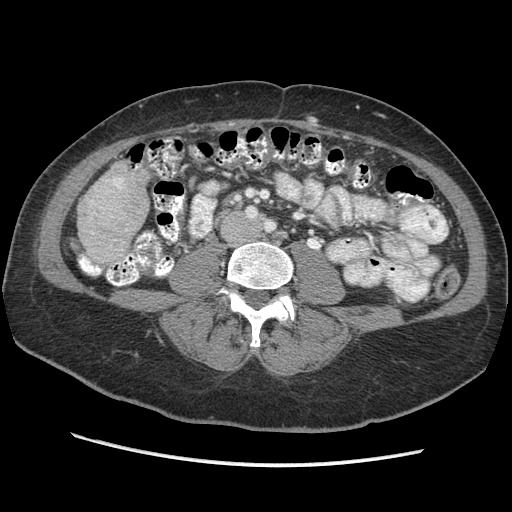
Contrast-enhanced abdominal CT (liver protocol), one axial slice. Slice 86 of 170 in the series (ordered by position). Soft-tissue window (W 400 / L 40 HU). 2.5 mm slice thickness. 512 × 512 image matrix. Case-level facts recorded for this patient, not image findings: diagnosis: hepatocellular carcinoma (patient treated with transarterial chemoembolisation; whether this scan precedes or follows treatment is not stated here); TNM stage (as recorded): Stage-II; Child-Pugh class: A; tumour differentiation: no biopsy; tumour nodularity: multinodular.
Structures marked on this image (semi-automatic segmentation, software-assisted and operator-edited):
- liver parenchyma outside the tumour (the mass and vessels are separate outlines, so this box may not span the whole liver): bounding box [x1, y1, x2, y2] px = [76, 164, 148, 264]
- liver vessels: [106, 178, 123, 189]